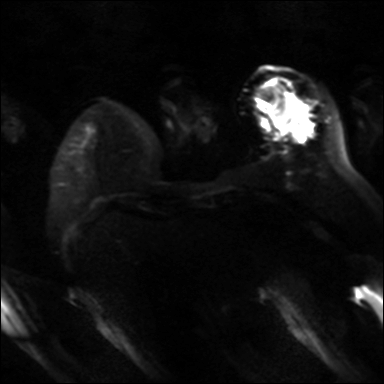
Breast MRI, one axial slice. Diffusion-weighted series; image 2 of 4 stored at this slice position (different b-values; order by instance number). 3 T. 384 × 384 image matrix, field of view 320 × 320 mm. Female patient.
Structures marked on this image (outlined manually by an expert reader):
- tumour on diffusion-weighted imaging: box from (x=260, y=112) to (x=315, y=137) px